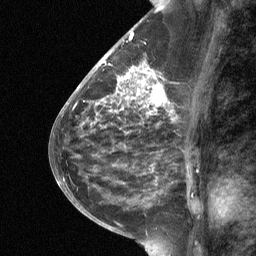
Breast MRI (dynamic contrast-enhanced), one sagittal slice; slice 29 of 64 in the series (ordered by position); dynamic contrast-enhanced study with each time point stored as its own series, time point 2 of 3 at this slice position (early post-contrast, ordered by acquisition time); 1.5 T; TE 4.8 ms, TR 27 ms; 256 × 256 image matrix, field of view 180 × 180 mm. Female patient, age 59 years. Case-level facts recorded for this patient, not image findings: setting: breast cancer imaged before/during neoadjuvant chemotherapy; receptor status: triple-negative.
Annotated regions visible in this slice (semi-automatically segmented with operator editing):
- analysis volume of interest (the breast-tissue region the enhancement analysis was run in; not a lesion): bounding box (x1, y1, x2, y2) in pixels: (113, 66, 169, 120)
- tumour enhancement mask (voxels above the 90 % enhancement threshold inside the analysis volume of interest): (118, 67, 163, 104)